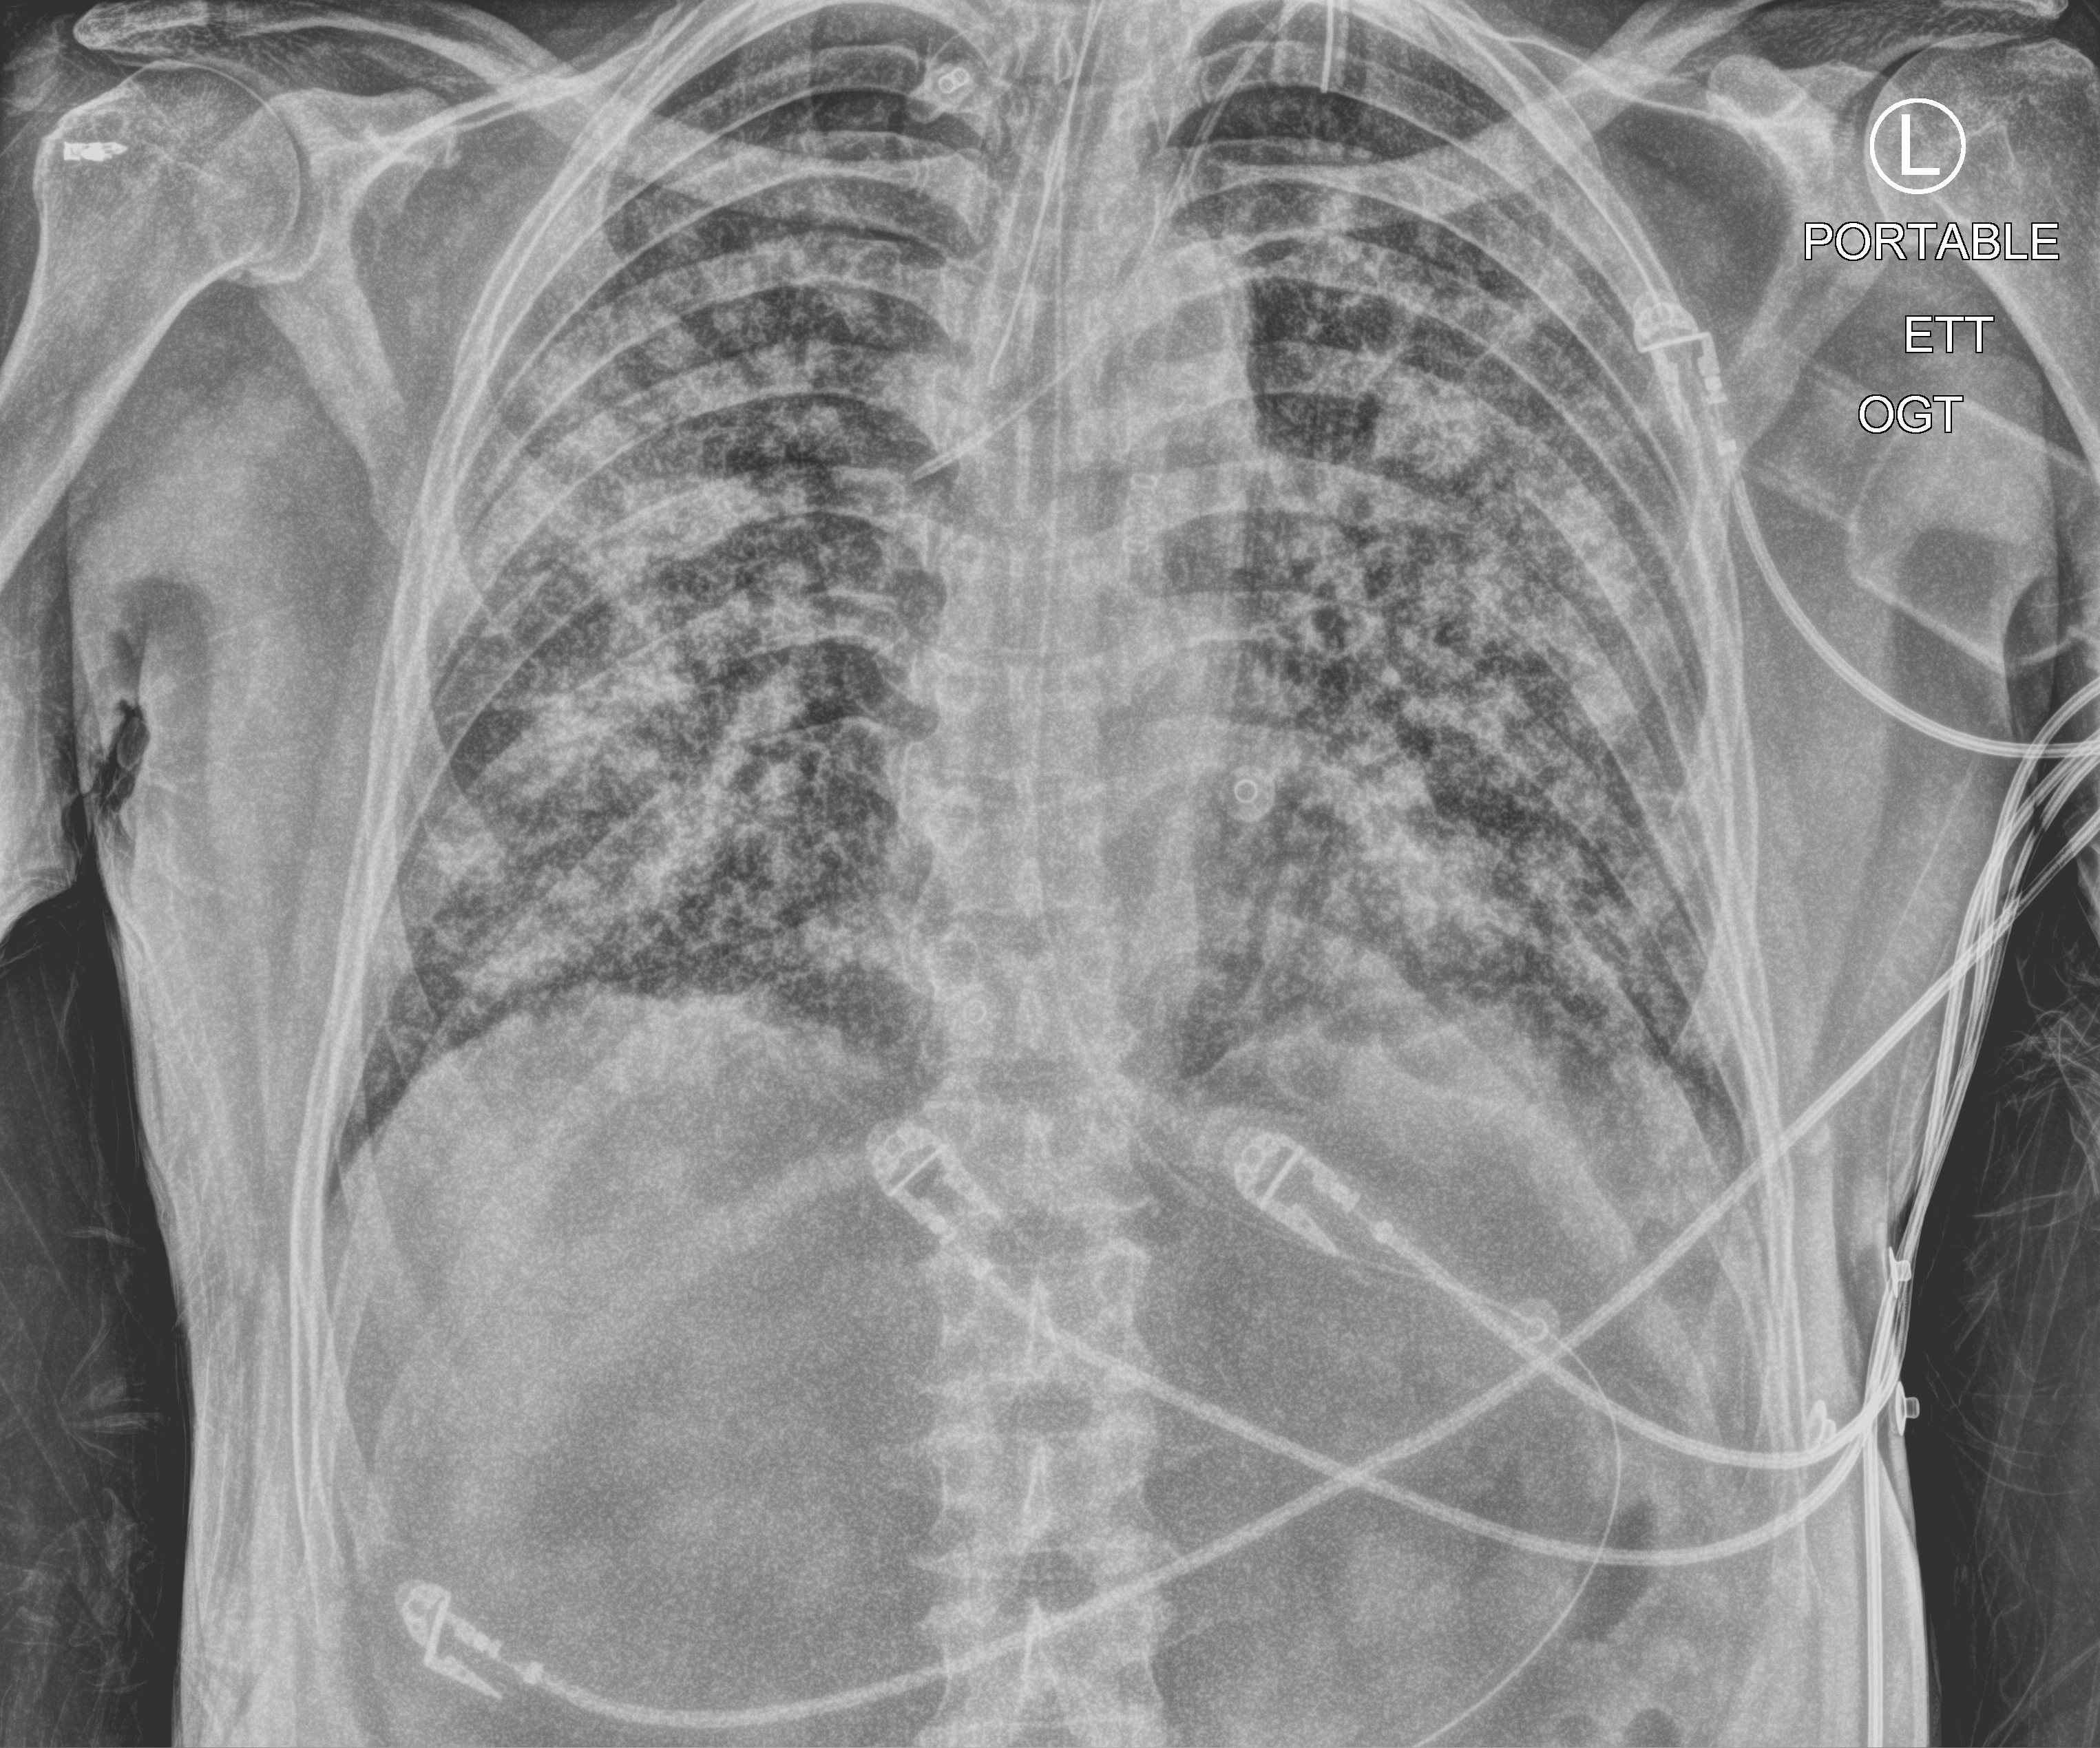
Portable chest radiograph. Patient hospitalised with COVID-19; male, aged 60–74 years.
Admission-level facts for this patient (not findings on this image; timing relative to this image not recorded):
- length of hospital stay: 65 days
- other chronic lung disease (admission record): yes